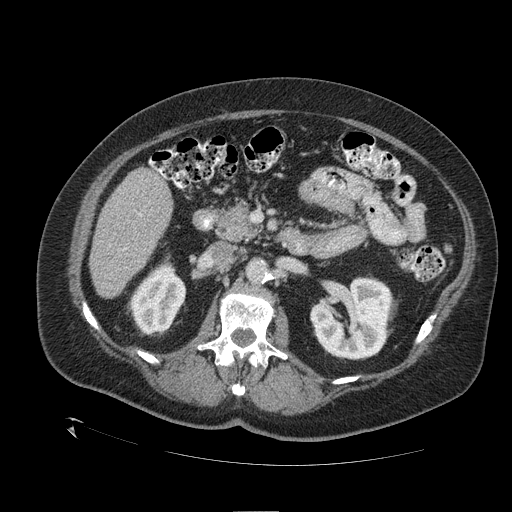
Contrast-enhanced abdominal CT (liver protocol), one axial slice. Position 50 of 109 along the scan axis. One of 2 acquisitions stored at this slice position. Soft-tissue window (W 400 / L 40 HU). 512 × 512 image matrix, field of view 460 × 460 mm. Case-level facts recorded for this patient, not image findings: diagnosis: hepatocellular carcinoma (patient treated with transarterial chemoembolisation; whether this scan precedes or follows treatment is not stated here); TNM stage (as recorded): Stage-I; Child-Pugh class: A; tumour differentiation: no biopsy; tumour nodularity: uninodular.
Structures marked on this image (semi-automatically segmented with operator editing):
- liver parenchyma outside the tumour (the mass and vessels are separate outlines, so this box may not span the whole liver): bounding box <90,168,172,298> (left, top, right, bottom; pixels)
- liver vessels: <123,169,165,250>